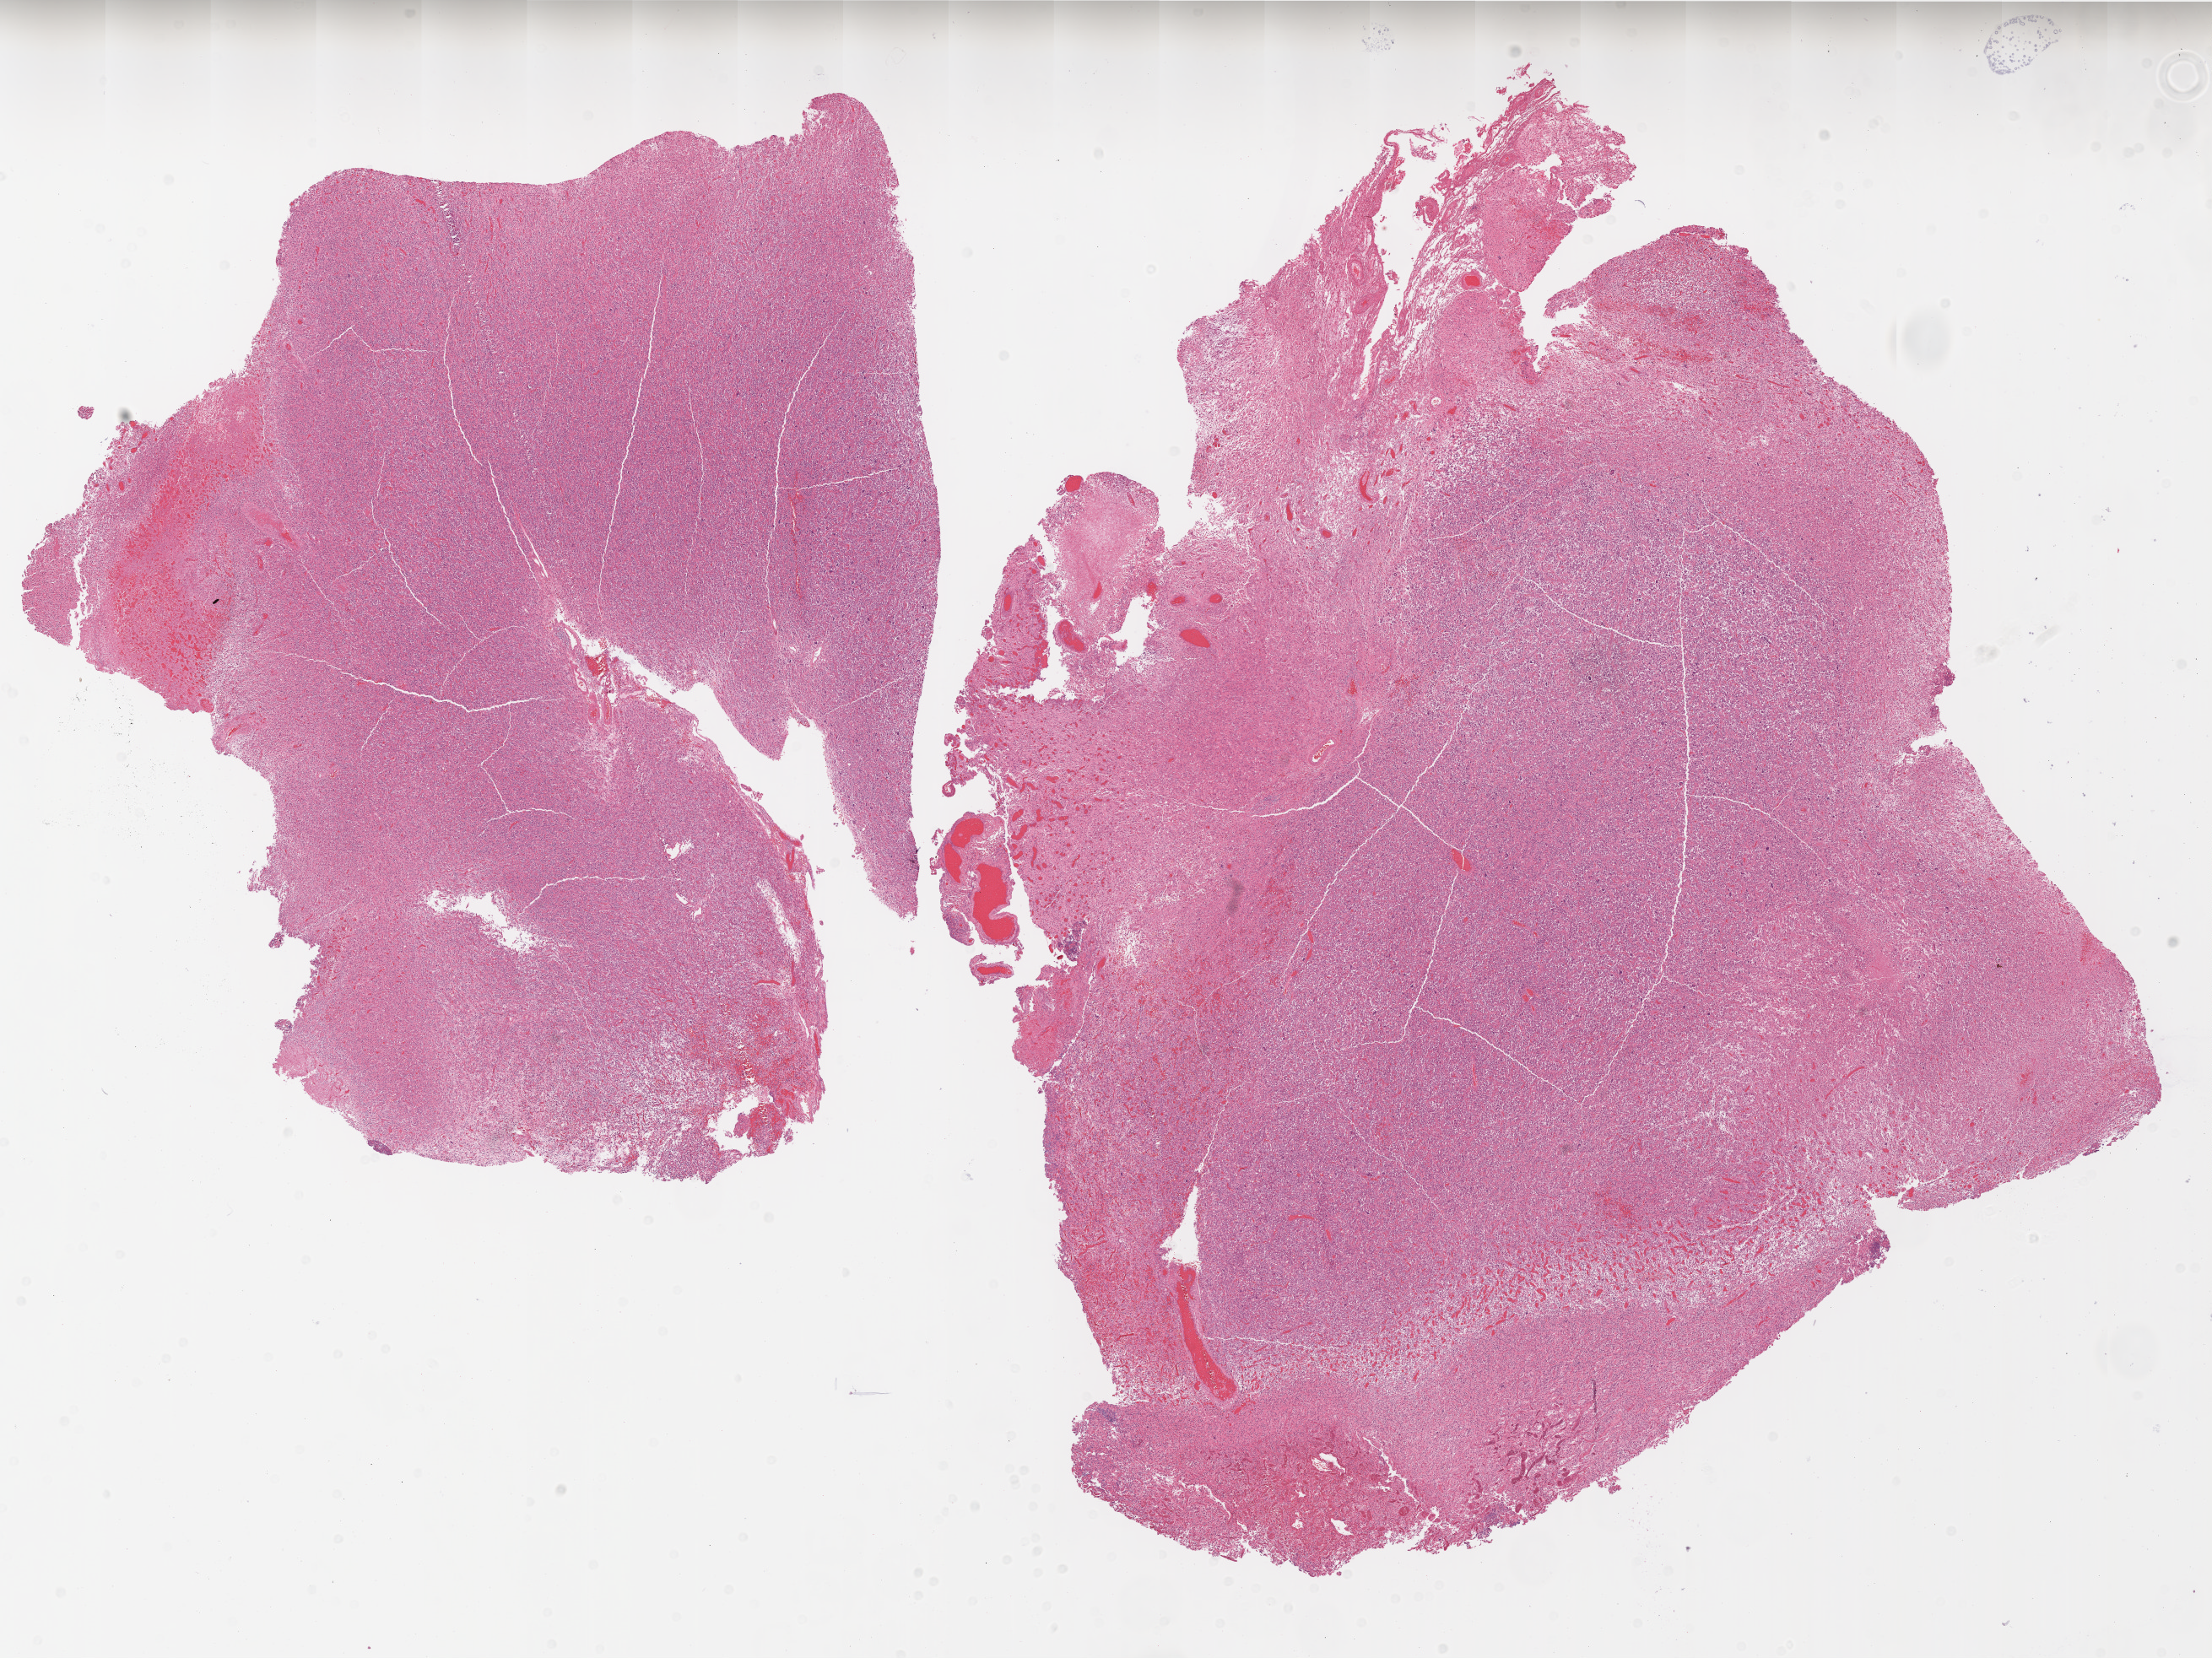
Digitized H&E-stained tissue section (whole slide), low-resolution overview of the scanned area, about 21.0 x 15.7 mm (from a 20x scan); FFPE section; sample: primary tumour, brain. Male patient; age at initial diagnosis 68 years.
Diagnosis: Glioblastoma.